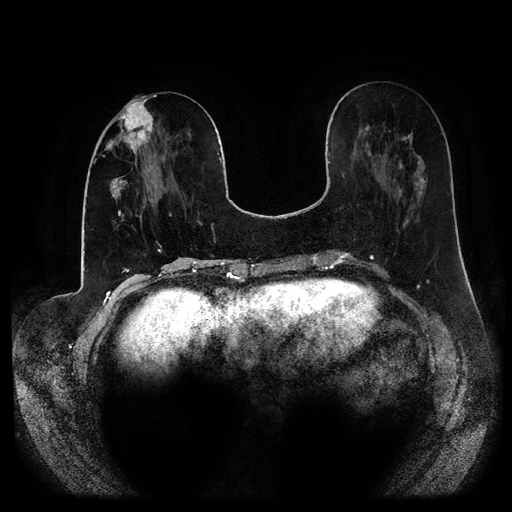
Breast MRI (dynamic contrast-enhanced, multi-phase), one axial slice. Slice 35 of 116 in the series (ordered by position). Dynamic contrast-enhanced series, time point 2 of 5 at this slice position (early post-contrast). 1.5 T. TE 2.6 ms, TR 5.2 ms. 2 mm slice thickness. 512 × 512 image matrix, field of view 380 × 380 mm. Female patient, age 53 years.
Annotated regions visible in this slice (semi-automatically segmented with operator editing):
- breast lesion (labelled 'tumour' in the annotation; benign lesions carry a separate 'benign' label): bounding box [x1, y1, x2, y2] px = [105, 98, 159, 155]